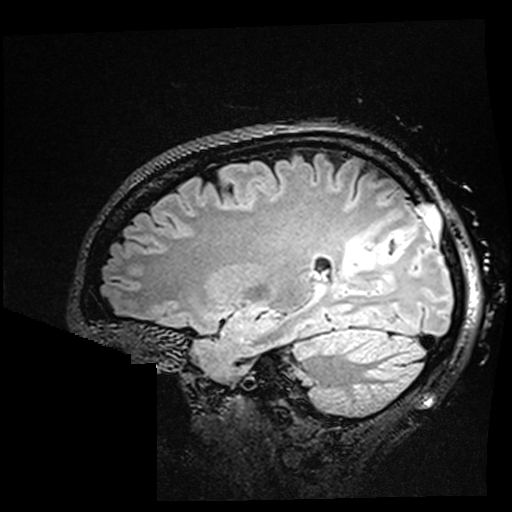
Brain MRI from a brain-tumour surgery series, one sagittal slice. Slice 116 of 176 in the series (ordered by position). T2 FLAIR. 1 mm slice thickness. 512 × 512 image matrix, field of view 250 × 250 mm. Case-level facts recorded for this patient, not image findings: histopathology: Oligodendroglioma; WHO grade: 2; IDH mutation: yes; tumour location: Right Parietal.
Outlined on this slice (outlined manually by an expert reader):
- residual tumour: bounding box (x1, y1, x2, y2) in pixels: (342, 234, 389, 280)